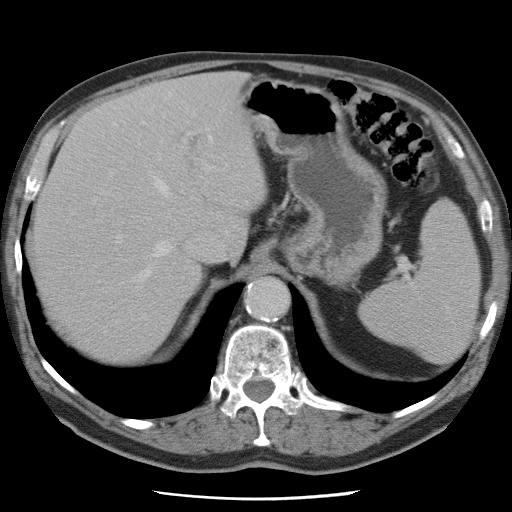
Contrast-enhanced abdominal CT, one axial slice; slice 56 of 78 in the series (ordered by position); intravenous contrast given; soft-tissue window (W 400 / L 40 HU); 5 mm slice thickness; 512 × 512 image matrix. Male patient, age 75 years. From the clinical record (not read from this slice): diagnosis: colorectal cancer liver metastases, imaged before liver resection; multiple liver metastases: yes.
Structures marked on this image (expert manual segmentation):
- hepatic veins: bounding box <93,127,211,282> (left, top, right, bottom; pixels)
- liver: <35,74,266,358>
- planned liver remnant (the part of the liver to remain after resection): <35,130,201,358>
- portal vein (with intrahepatic branches): <110,174,125,250>